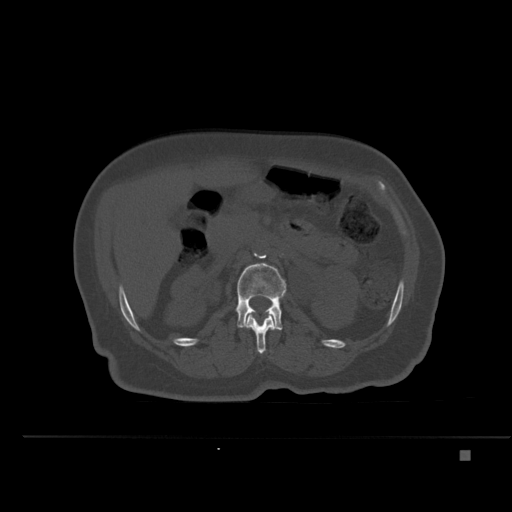
CT including the spine, one axial slice; bone window (W 1800 / L 400 HU); 1.5 mm slice thickness; 512 × 512 image matrix. Patient: female, 74 years. From the clinical record (not read from this slice): primary cancer: colon.
Outlined on this slice (semi-automatic segmentation, software-assisted and operator-edited):
- L1 vertebra: bounding box [x1, y1, x2, y2] px = [244, 312, 277, 354]
- L2 vertebra: [236, 263, 287, 330]